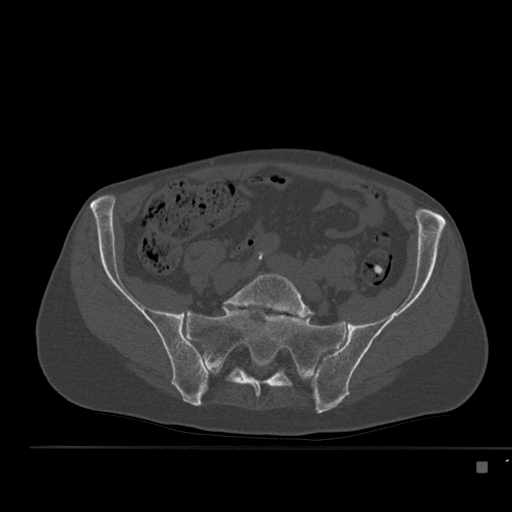
CT including the spine, one axial slice; slice 109 of 517 in the series (ordered by position); reconstruction kernel Br40s; bone window (W 1800 / L 400 HU); 1.5 mm slice thickness; 512 × 512 image matrix, field of view 408 × 408 mm. Male patient, age 70 years. Case-level facts recorded for this patient, not image findings: primary cancer: renal; vertebrae with lytic lesions (as recorded): T4, T6, T10, T12, L3, L4, L5.
Outlined on this slice (semi-automatically segmented with operator editing):
- L5 vertebra: box from (x=223, y=273) to (x=313, y=319) px